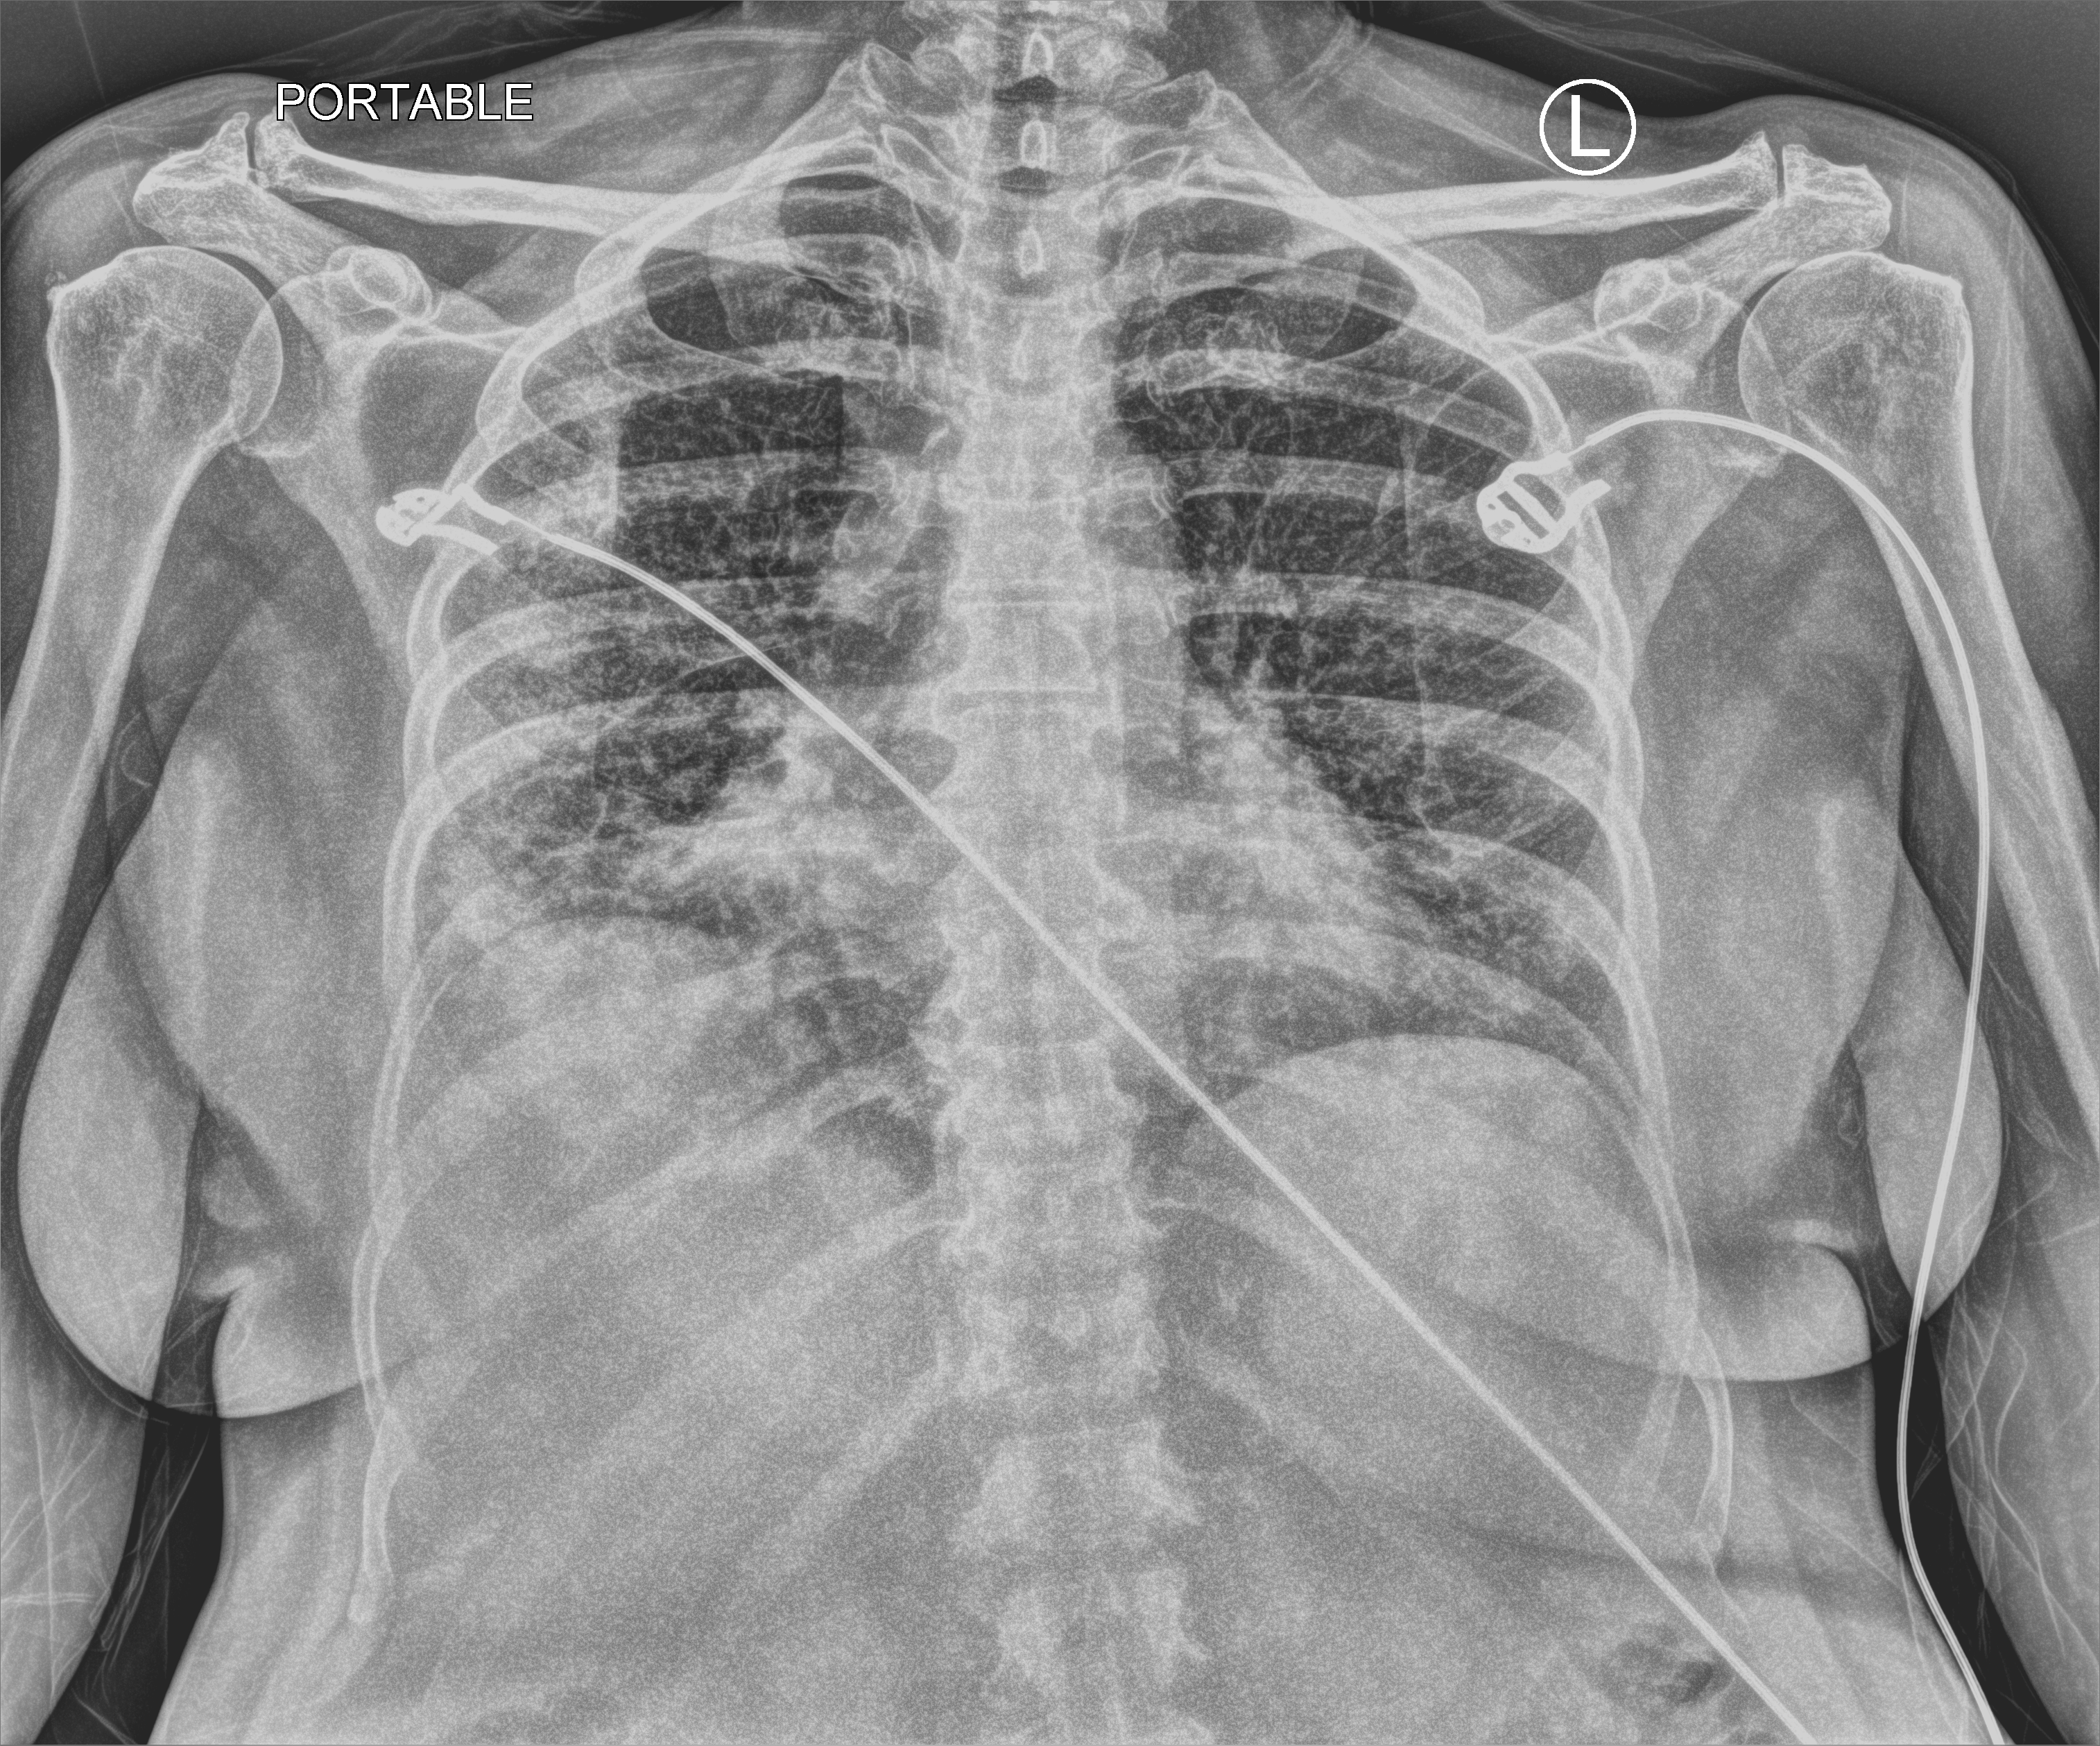
Chest X-ray (portable); anteroposterior (AP) projection. Female patient hospitalised with COVID-19, age 60–74 years.
From the hospital-stay record, not from the radiograph (when in the stay this image was taken is not recorded): hypertension (admission record): yes; chronic kidney disease (admission record): yes.